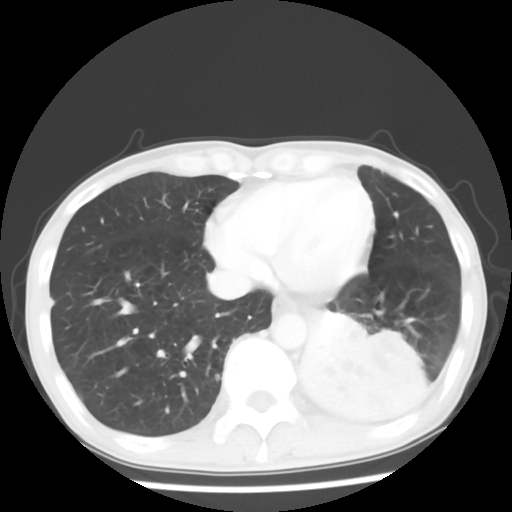
Chest CT, one axial slice. Slice 17 of 64 in the series (ordered by position). 120 kVp. Lung window (W 1500 / L -600 HU). 512 × 512 image matrix, field of view 313 × 313 mm. Male patient, age 68 years. From the clinical record (not read from this slice): clinical TNM (as recorded): T4 N0 M0.
Outlined on this slice (bounding box drawn by a radiologist):
- lung tumour (recorded histology: squamous cell carcinoma): bounding box (x1, y1, x2, y2) in pixels: (304, 311, 407, 420)